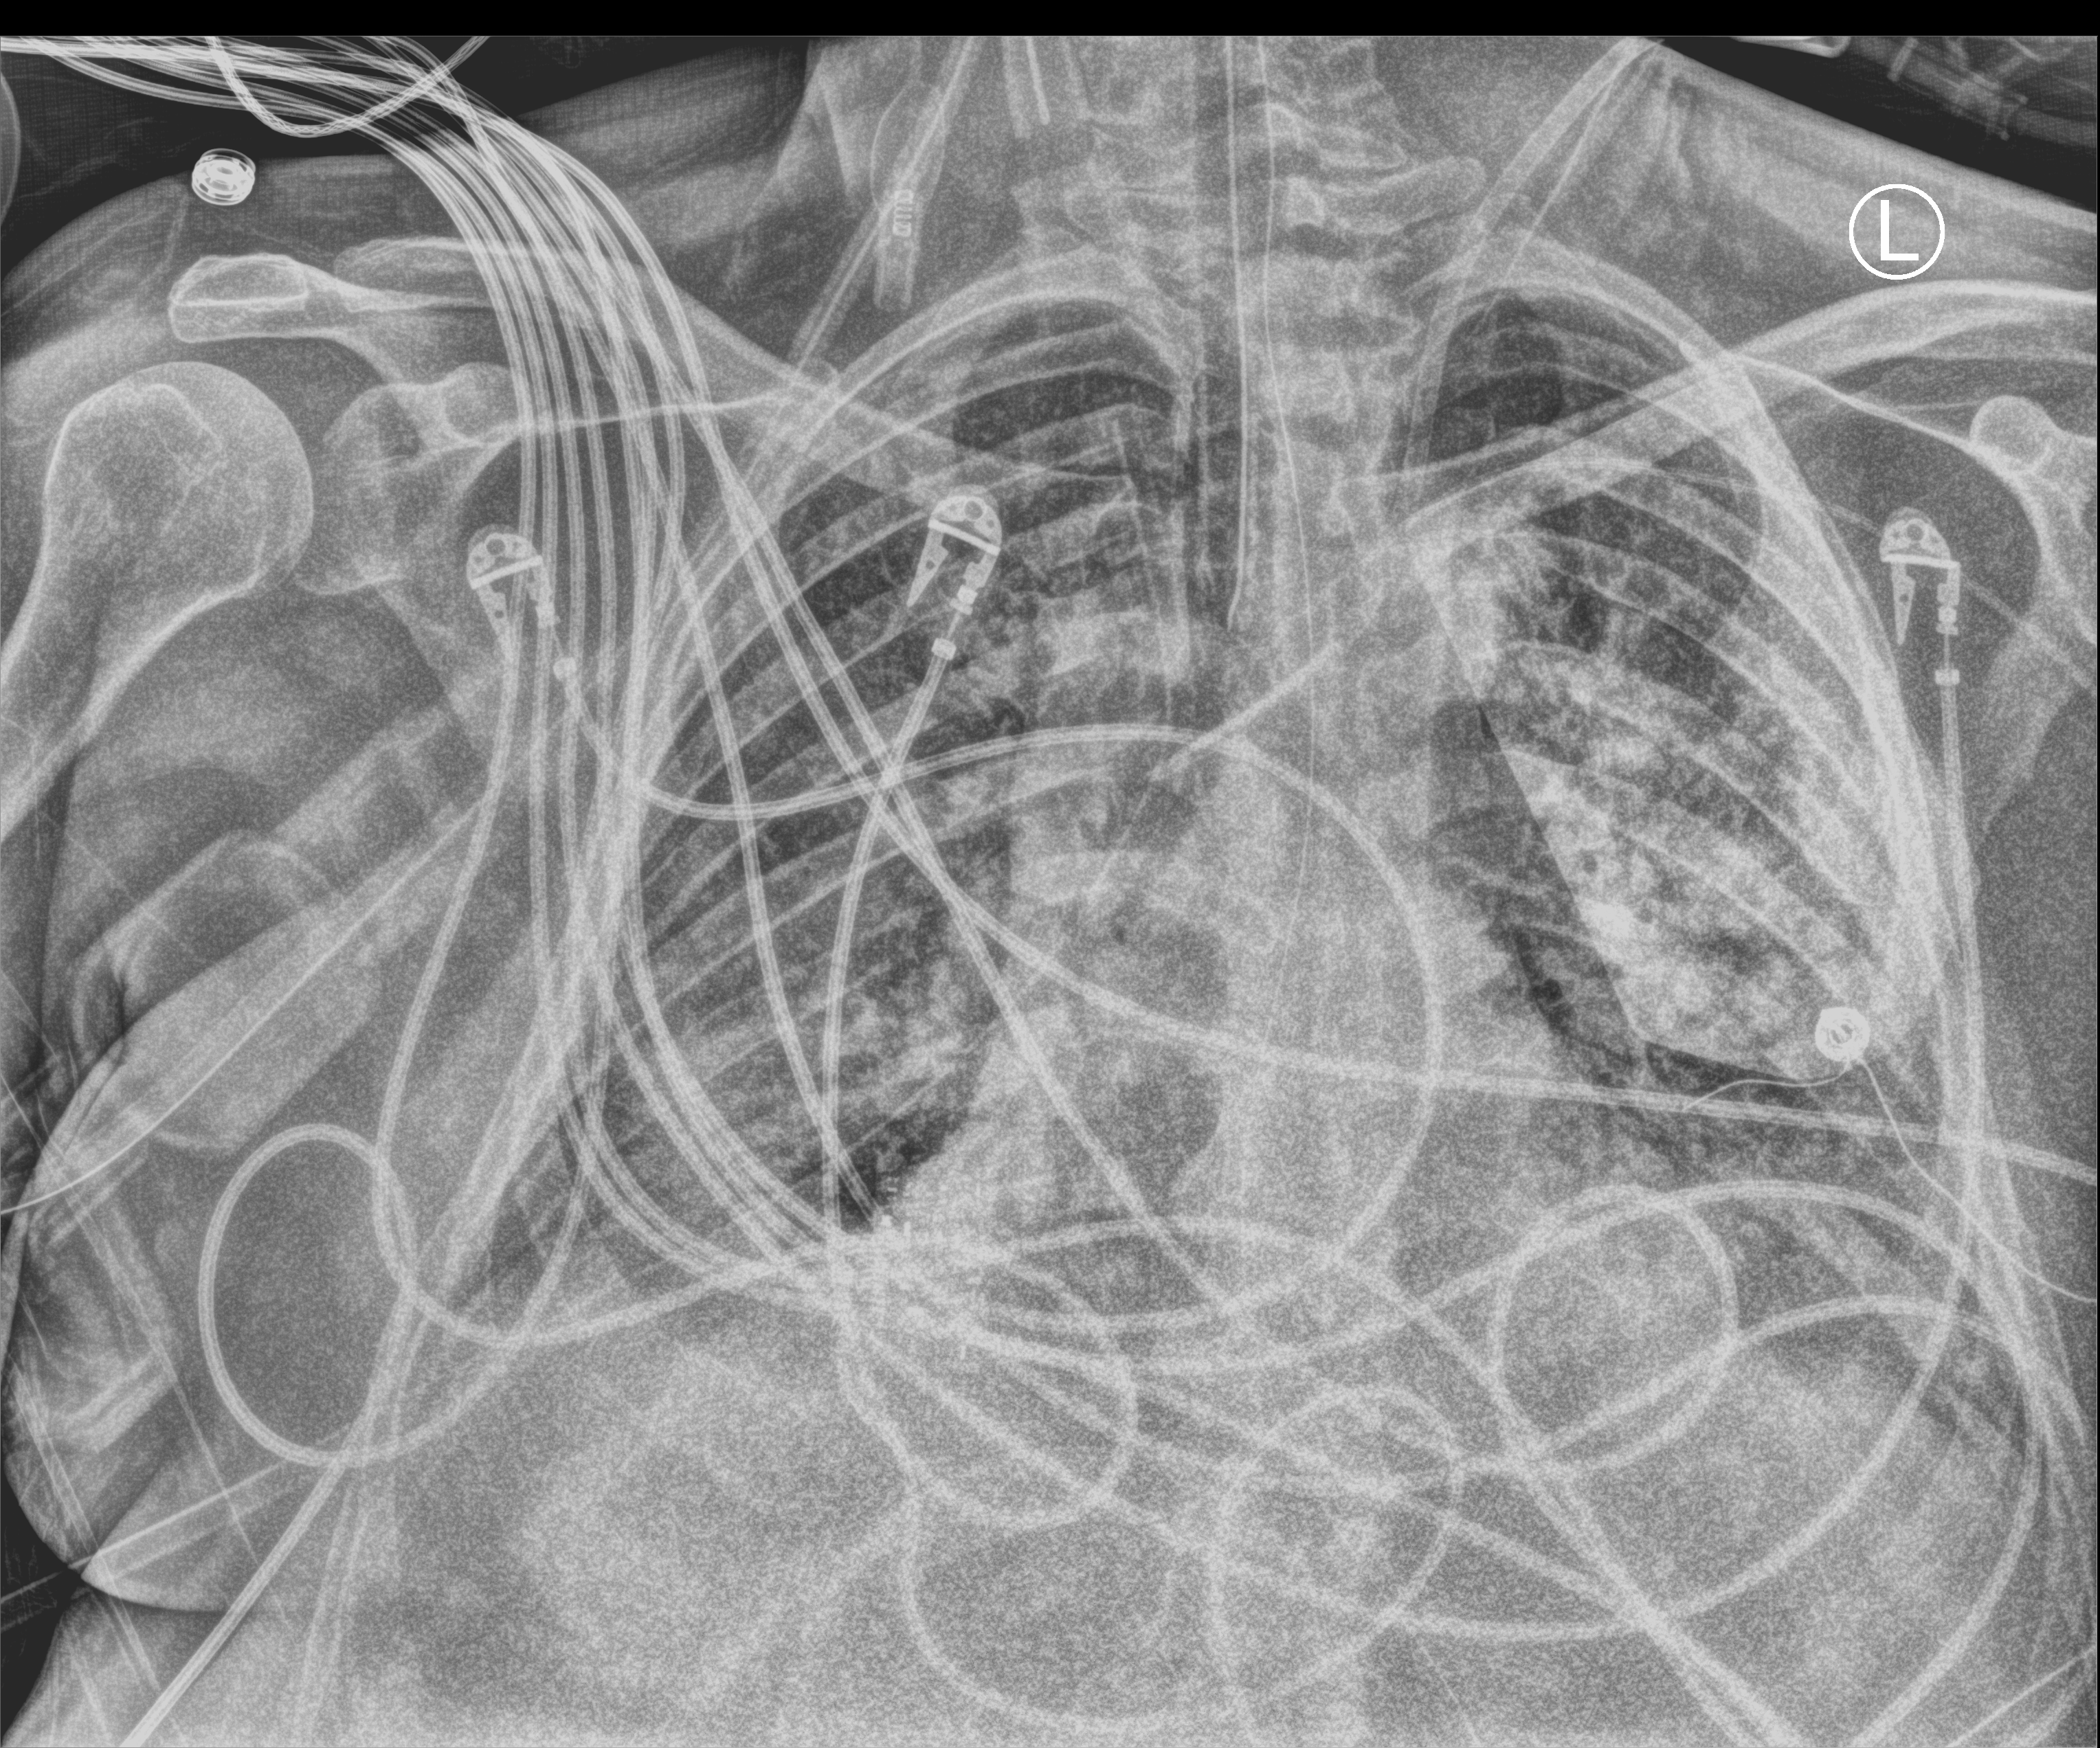
Chest X-ray (portable). Patient hospitalised with COVID-19; male, aged 18–59 years.
Hospital-stay facts (about this admission, not read from this image; timing relative to this image not recorded): admitted to intensive care during this hospital stay: yes; length of hospital stay: 39 days.